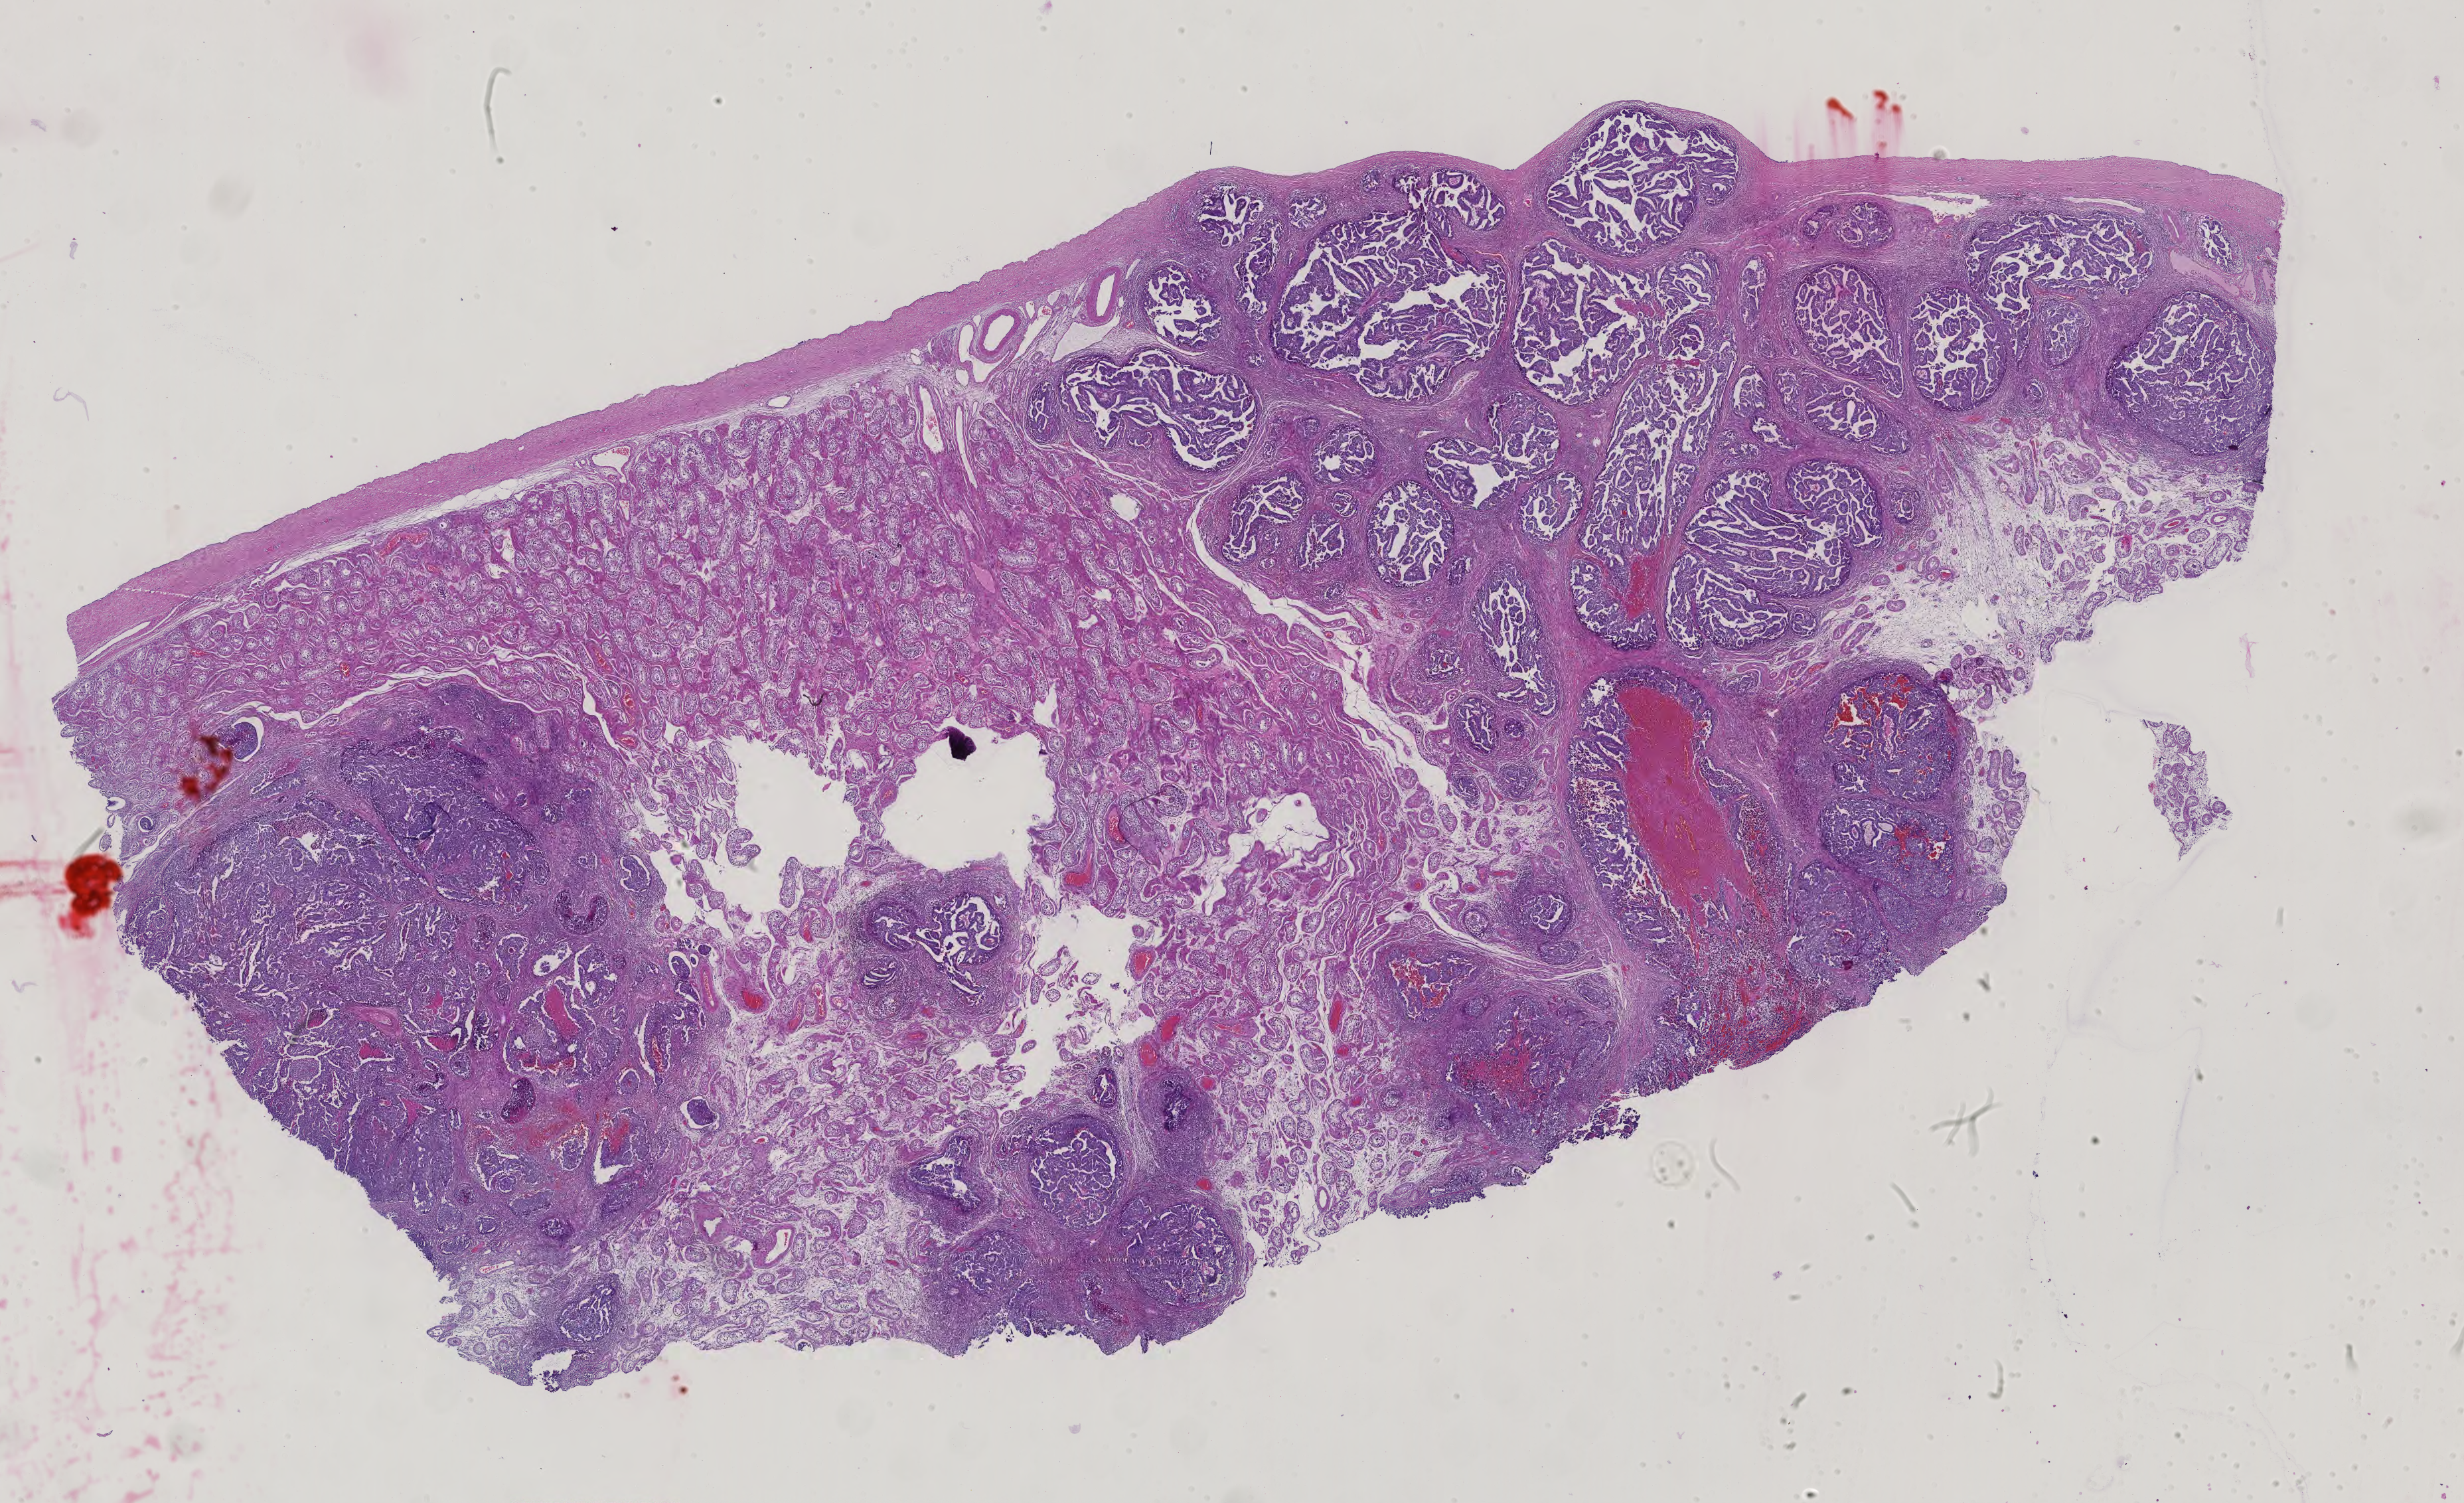
Whole-slide histology image, H&E-stained — shown as a low-resolution overview of the whole scanned area (about 27.0 x 16.5 mm, from a 40x scan), formalin-fixed paraffin-embedded (FFPE) diagnostic section, sample: primary tumour, testis. Patient: male, age at initial diagnosis 23 years.
Diagnosis: Mixed germ cell tumor. AJCC pathologic stage: IS. Laterality: bilateral.